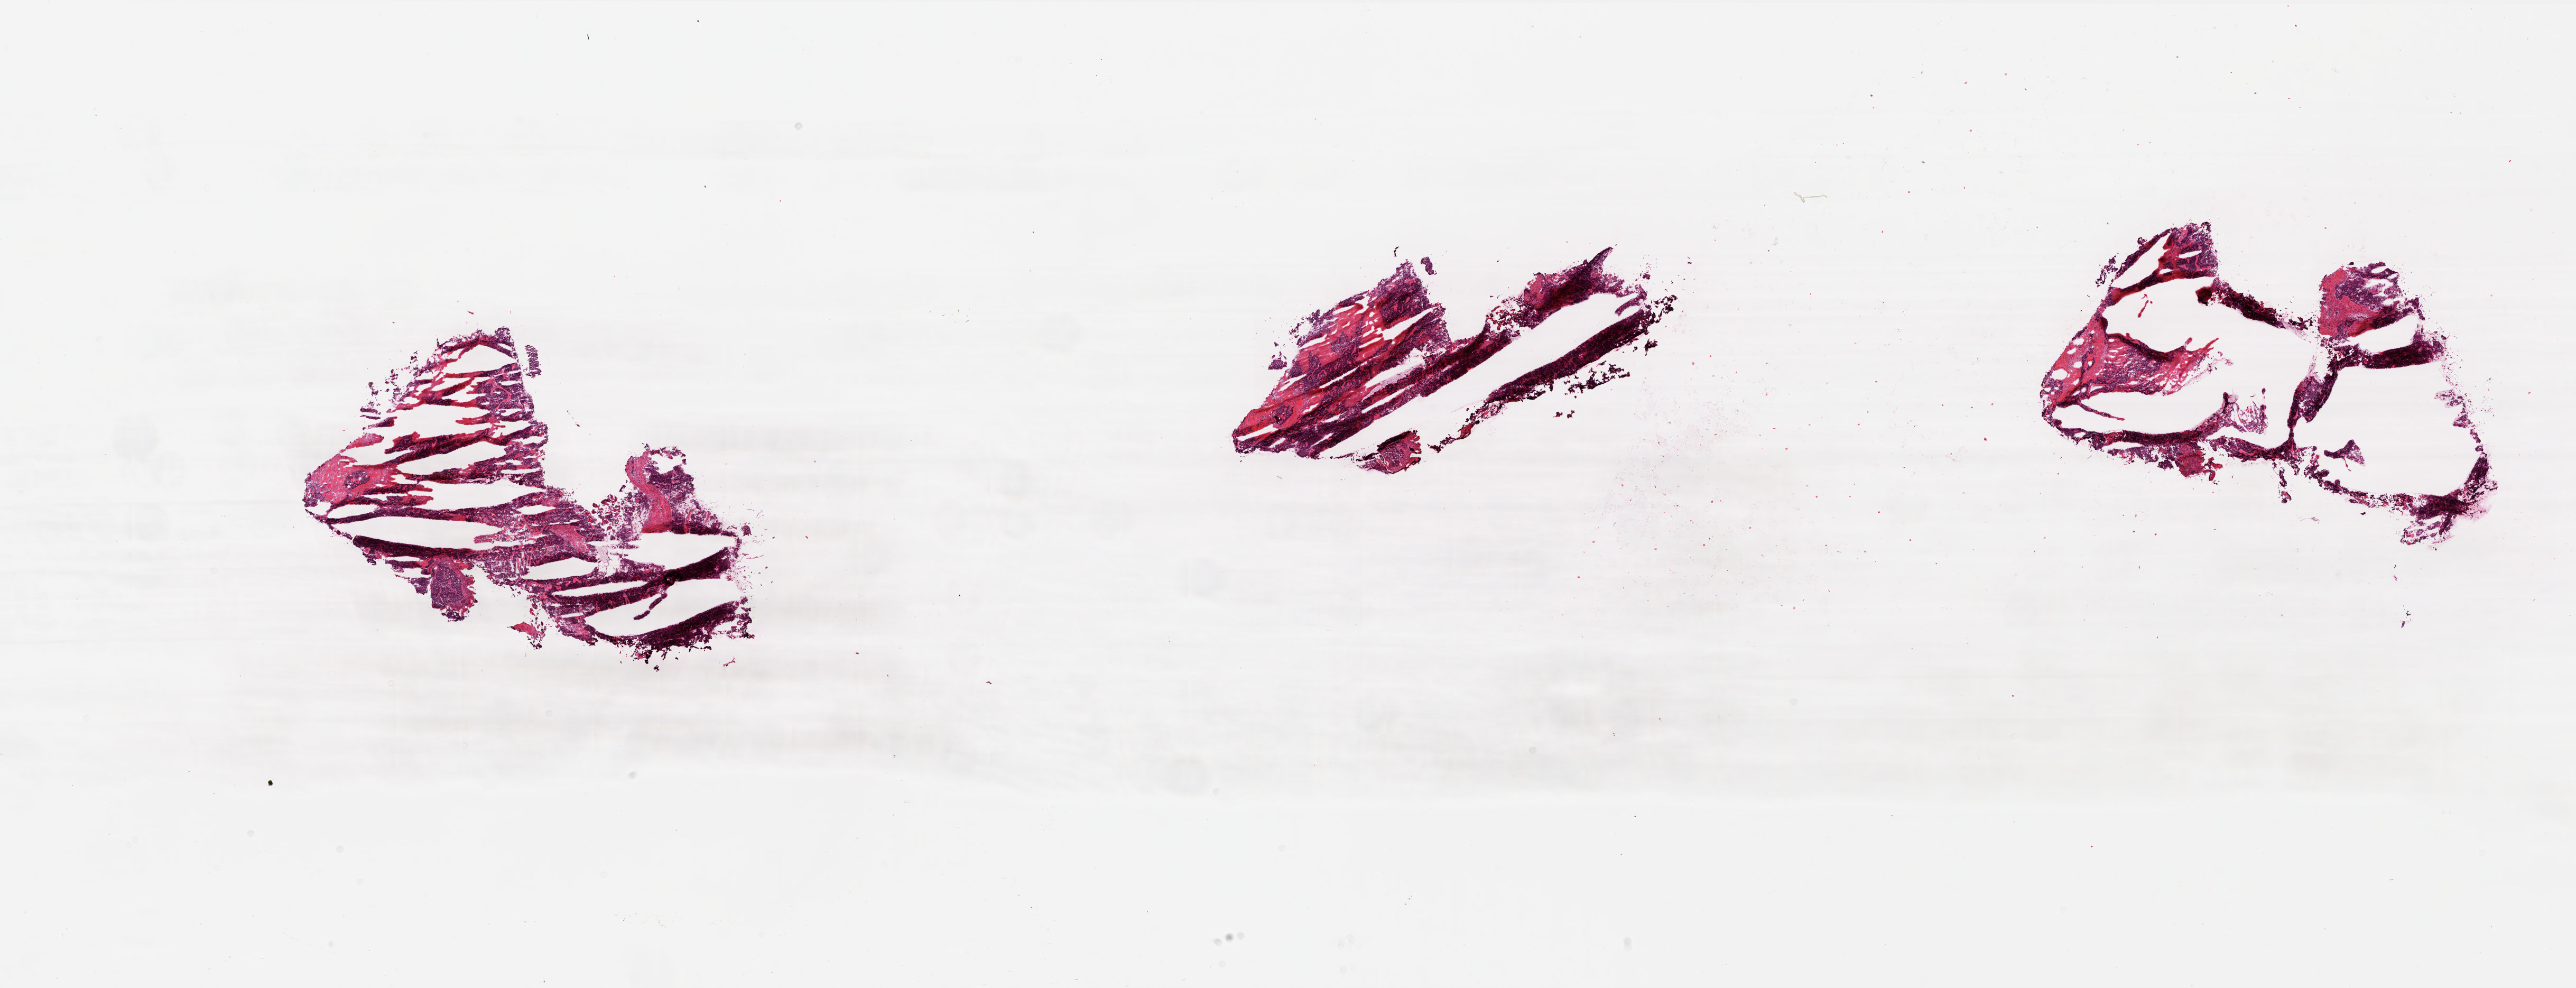
H&E whole-slide image — whole scanned area (about 38.9 x 14.9 mm, slide scanned at 20x) shown as a low-resolution overview, frozen section, sample: primary tumour, ovary. Patient: female, age at initial diagnosis 81 years. Histologic grade: G3 (poorly differentiated). Pathologist review of this section (percent, as recorded): tumour cells 93%, tumour nuclei 99%, normal cells 0%, stromal cells 5%, necrosis 2%.
• diagnosis: Serous cystadenocarcinoma, NOS
• FIGO stage: IV
• laterality: bilateral